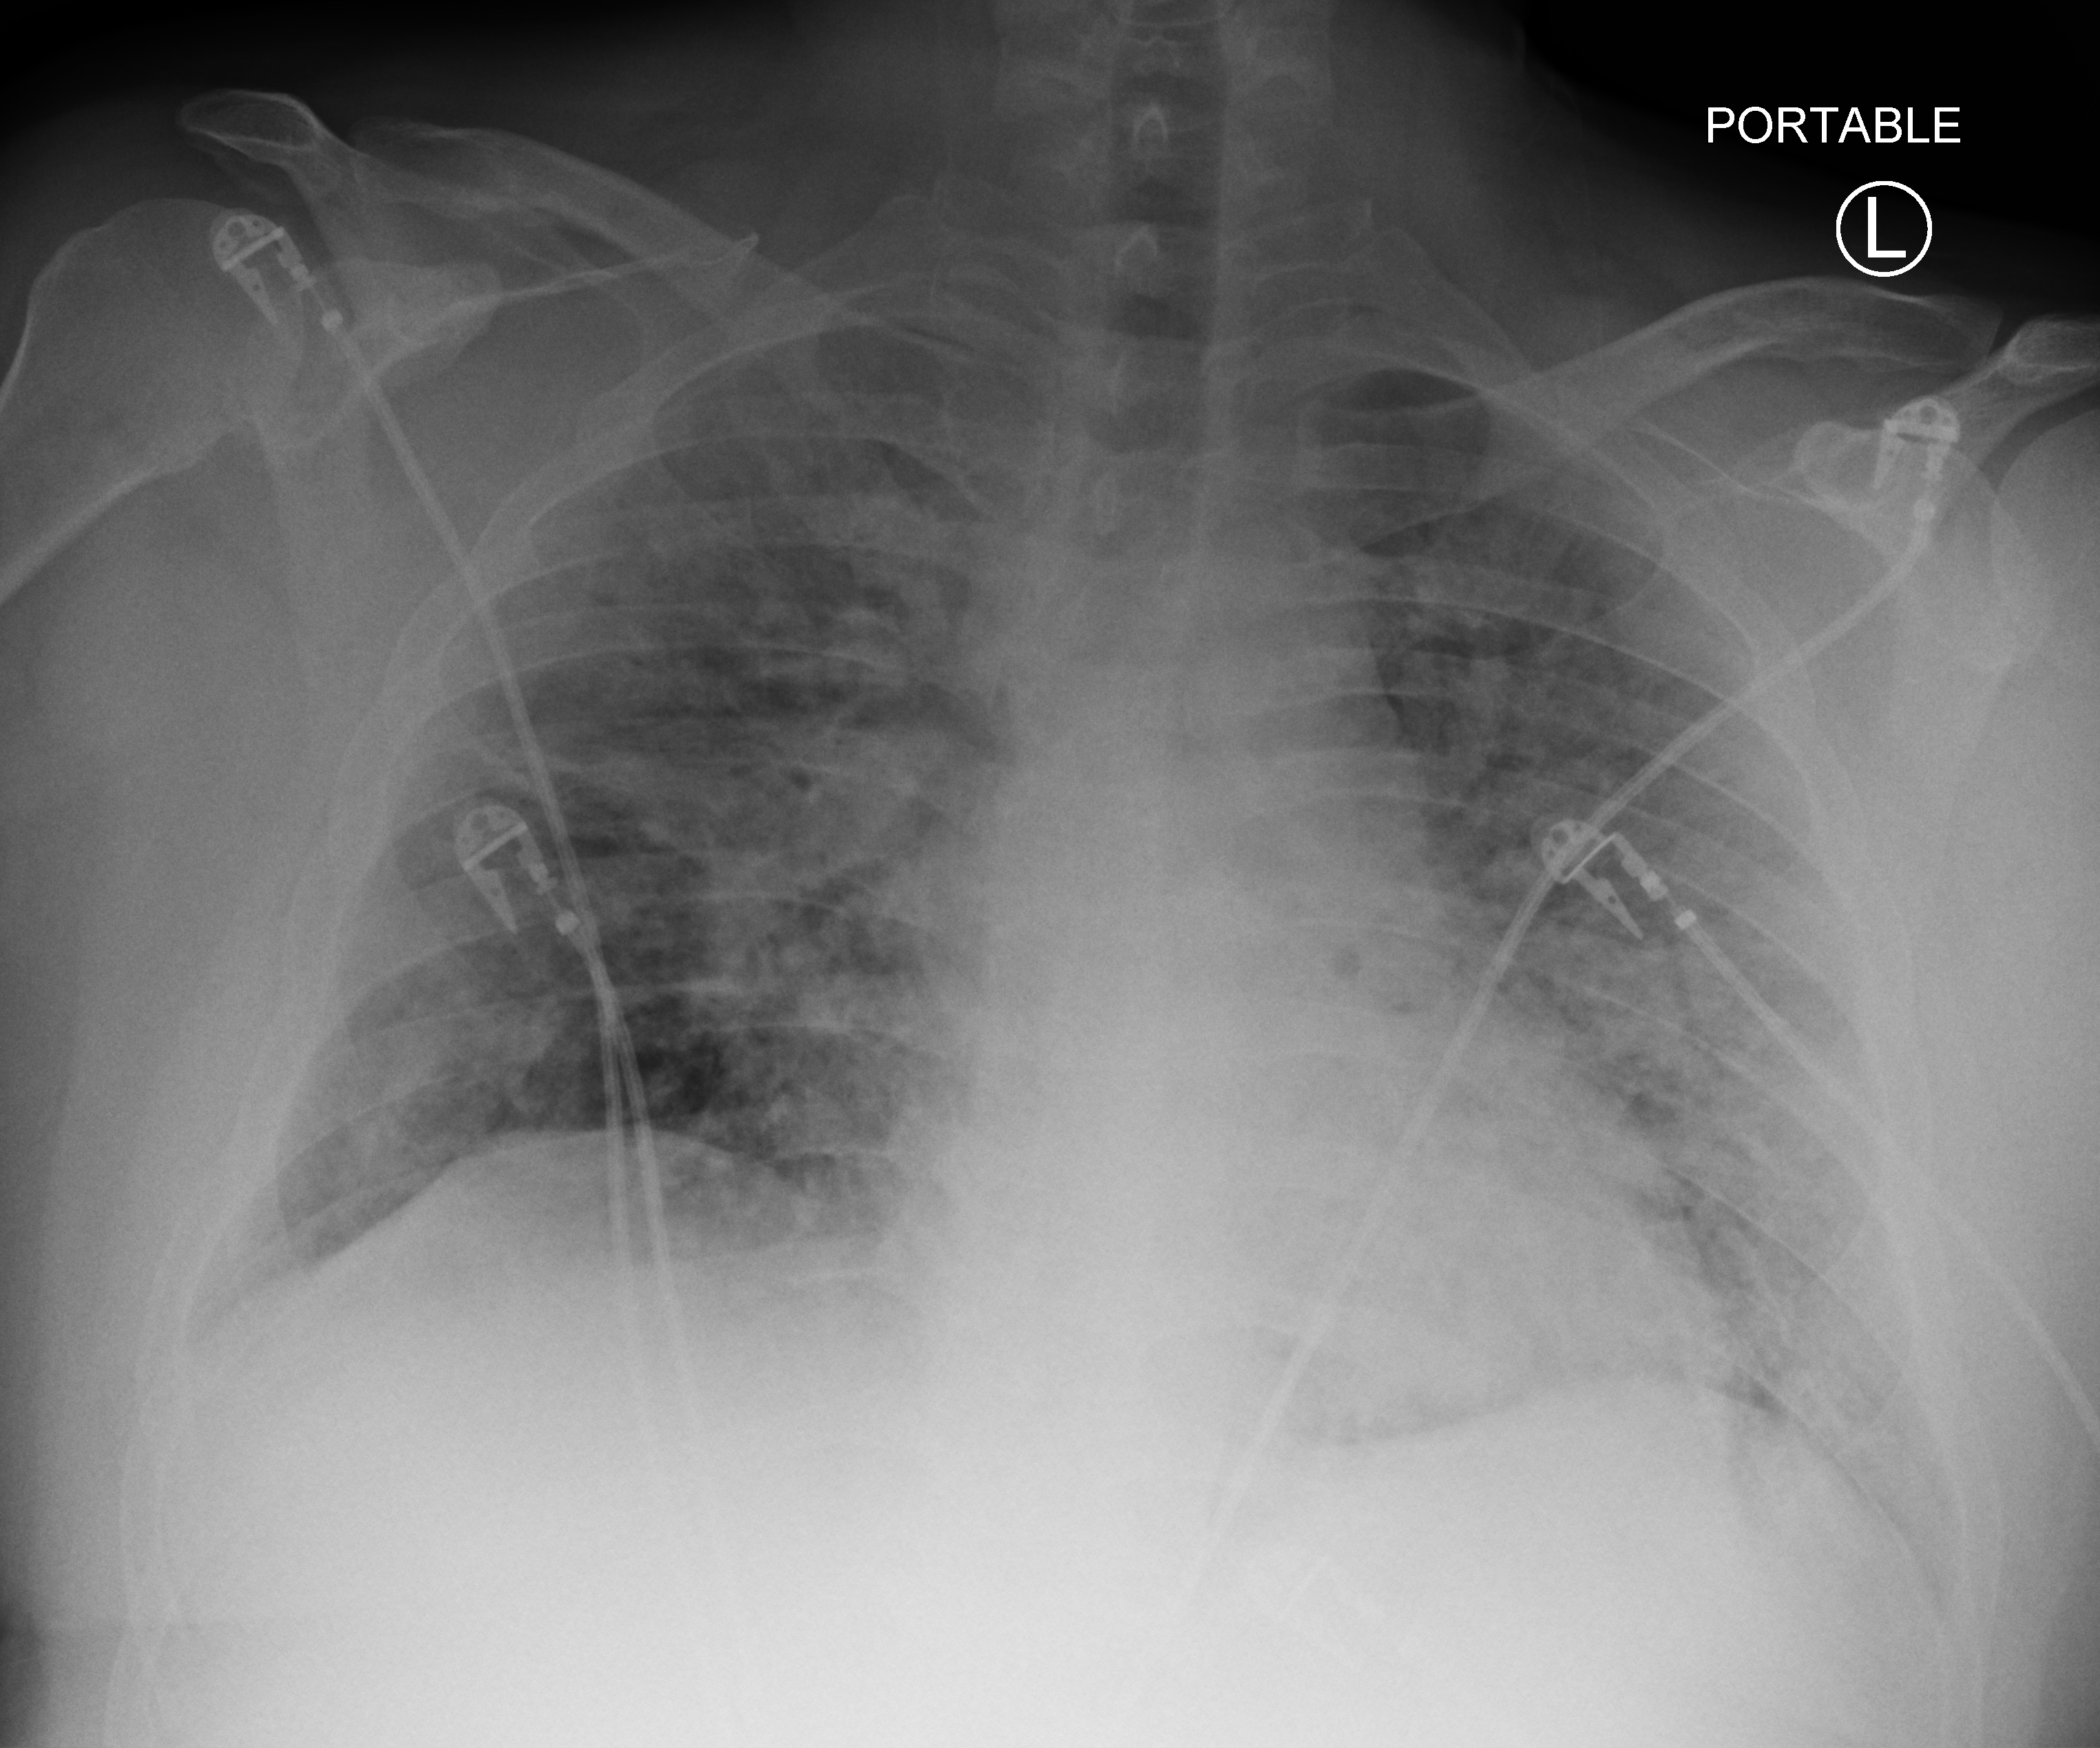
Chest X-ray (portable). Patient hospitalised with COVID-19, aged 18–59 years.
Hospital-stay facts (about this admission, not read from this image; timing relative to this image not recorded):
- mechanically ventilated during this hospital stay: yes
- admitted to intensive care during this hospital stay: yes